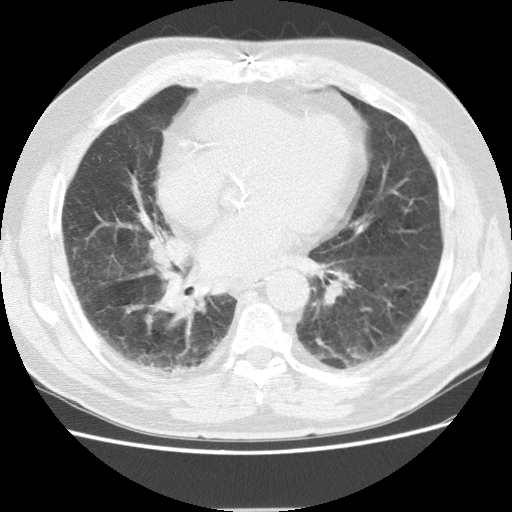
Axial slice from a low-dose chest CT screening exam, baseline annual screen, lung window (W 1500 / L -600 HU), standard (soft-tissue) reconstruction kernel (STANDARD), 512 × 512 image matrix. Male, age 72 years at enrolment. Former smoker at enrolment.
Expert-annotated lung lesion, bounding box <143,228,196,267> (left, top, right, bottom; pixels). No non-calcified nodule or mass ≥4 mm was recorded by the screening reader at this exam. Lung cancer was diagnosed 163 days after this screen: adenocarcinoma, NOS, right middle lobe, stage IIIB (AJCC 6th edition), 27 mm at pathology.